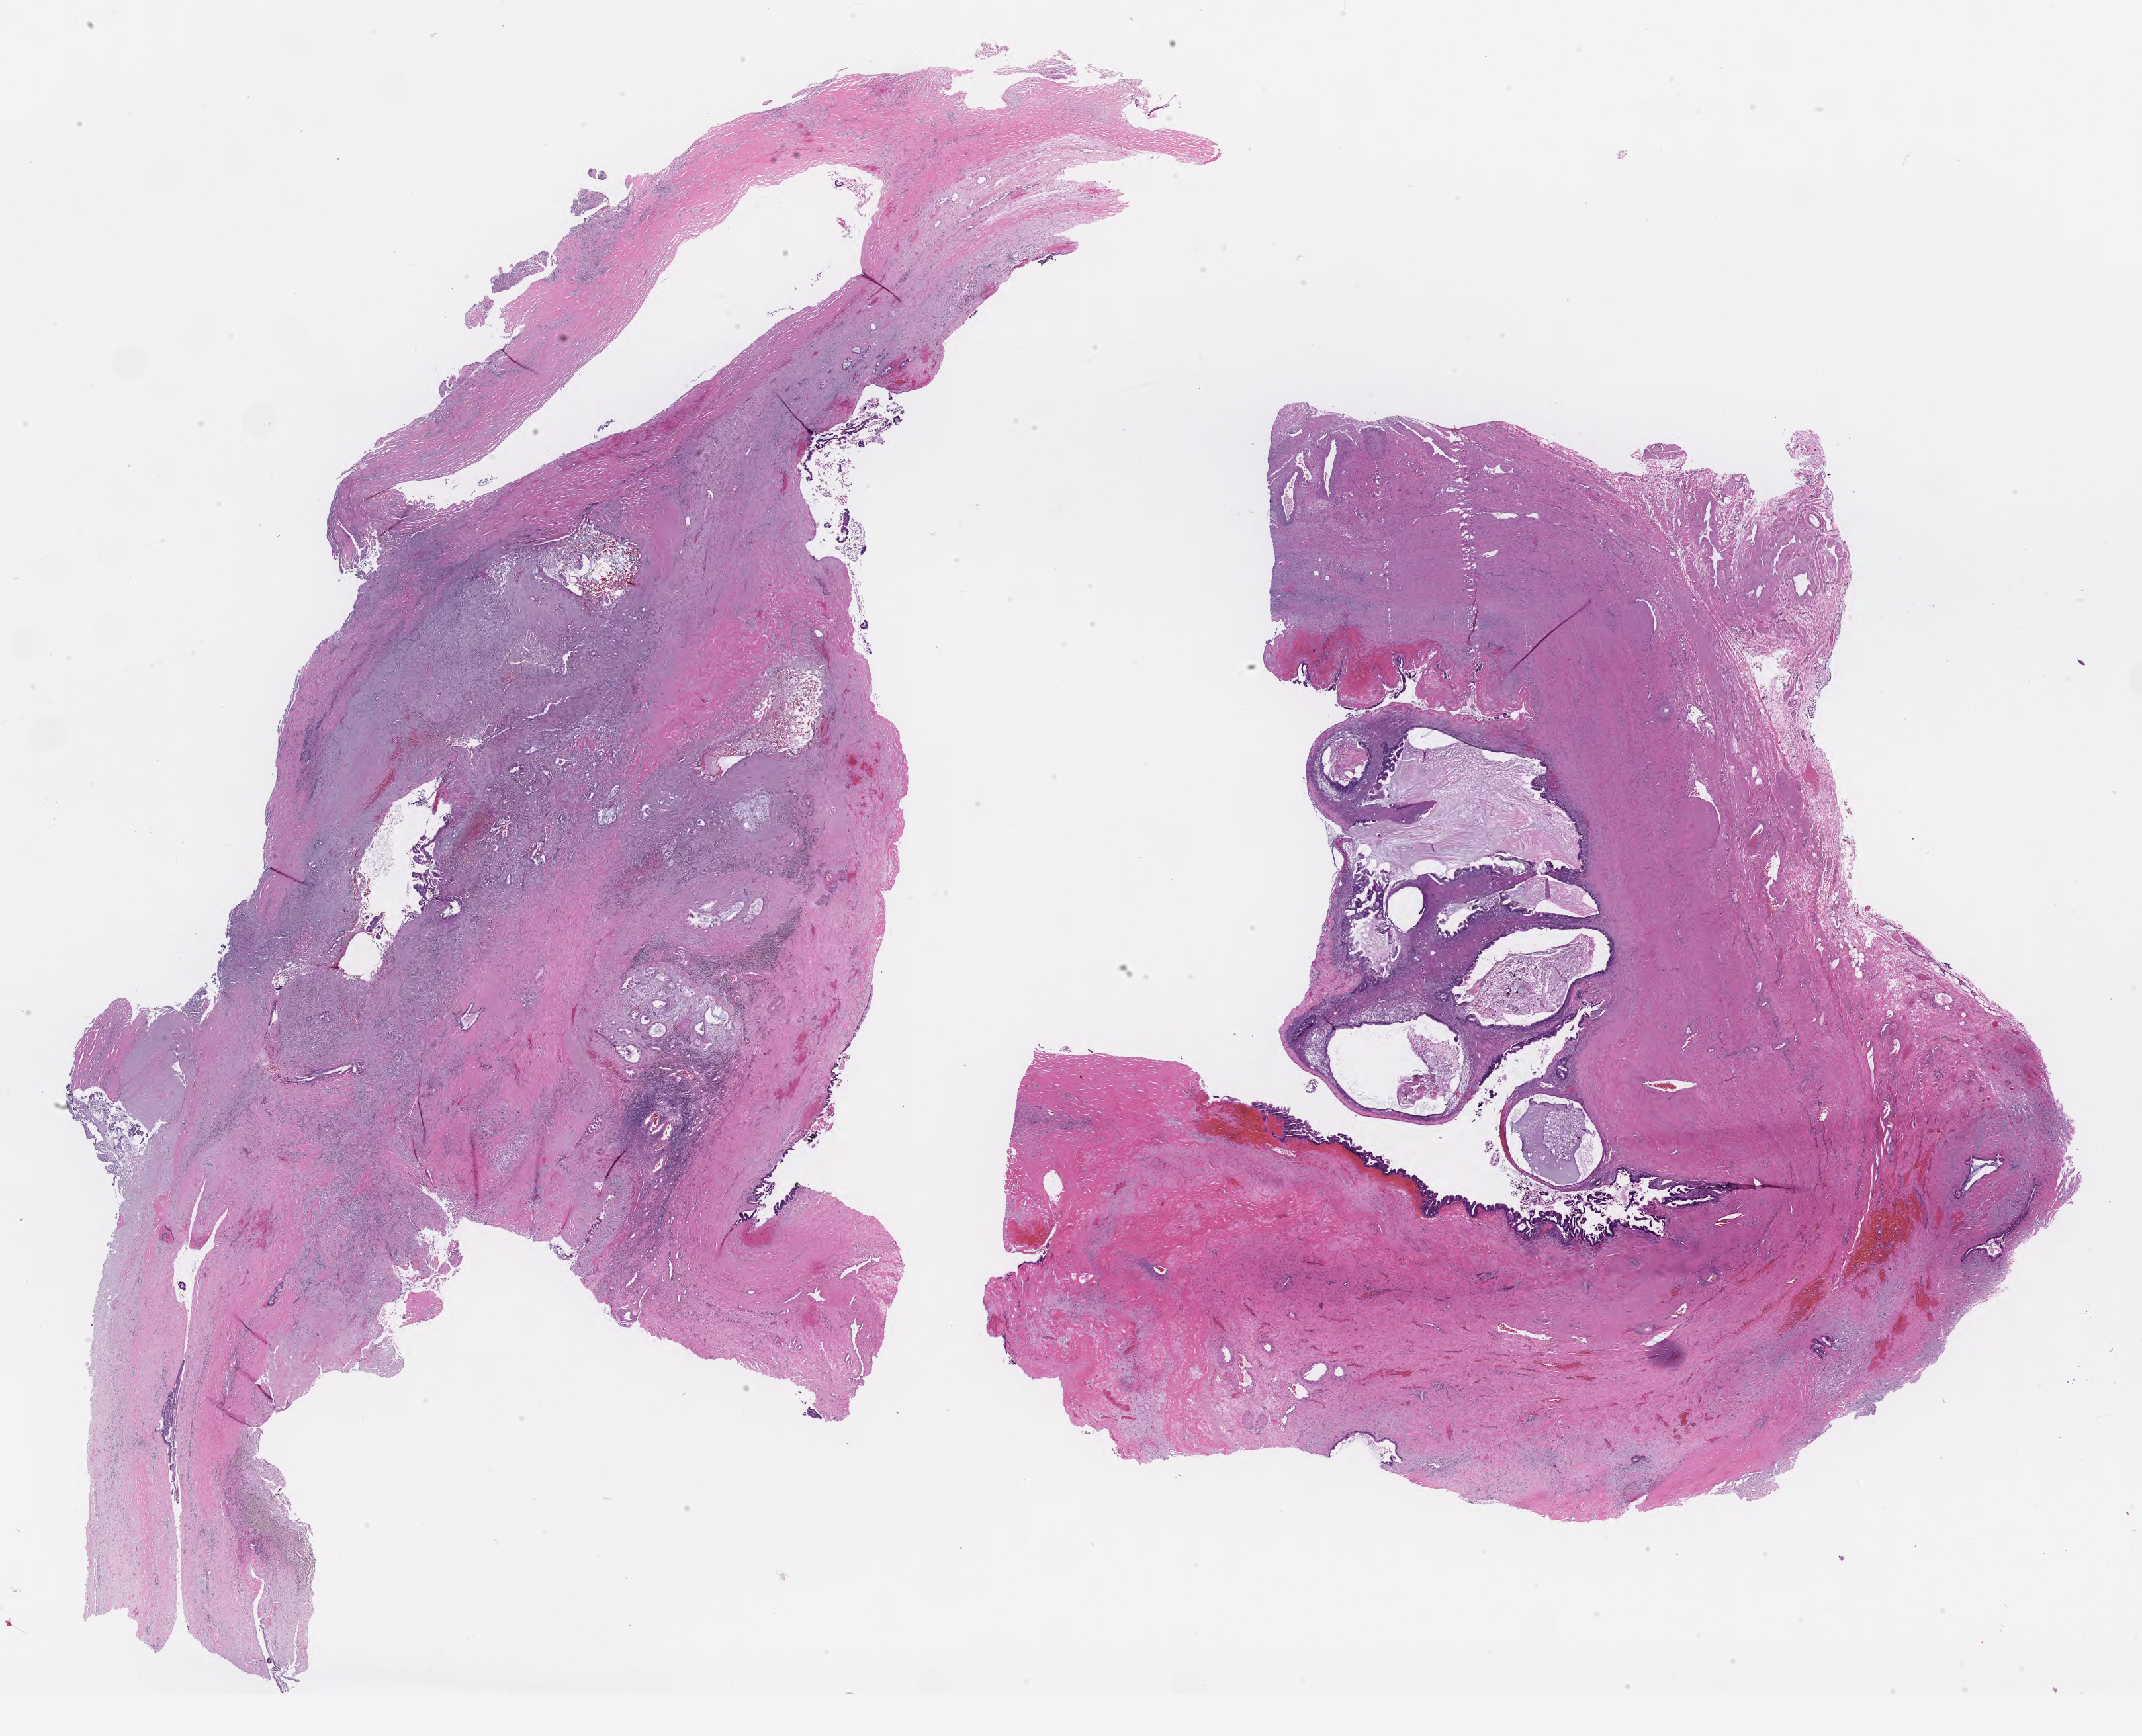
Whole-slide image, H&E stain — a low-resolution overview of the entire scanned area, about 26.1 x 21.2 mm, formalin-fixed paraffin-embedded section, specimen: primary tumor, site: ovary (right). Female patient; age at initial diagnosis 32 years. Composition of this section per pathologist review: tumor cells 50%, tumor nuclei 50%, stromal cells 45%, necrosis 2%, normal cells 3%. Inflammatory infiltration, as recorded: lymphocyte infiltration 6%, monocyte infiltration 20%, neutrophil infiltration 8%.
• AJCC pathologic stage: Stage IIIA2
• section: top of the tissue portion
• diagnosis: Mucinous adenocarcinoma